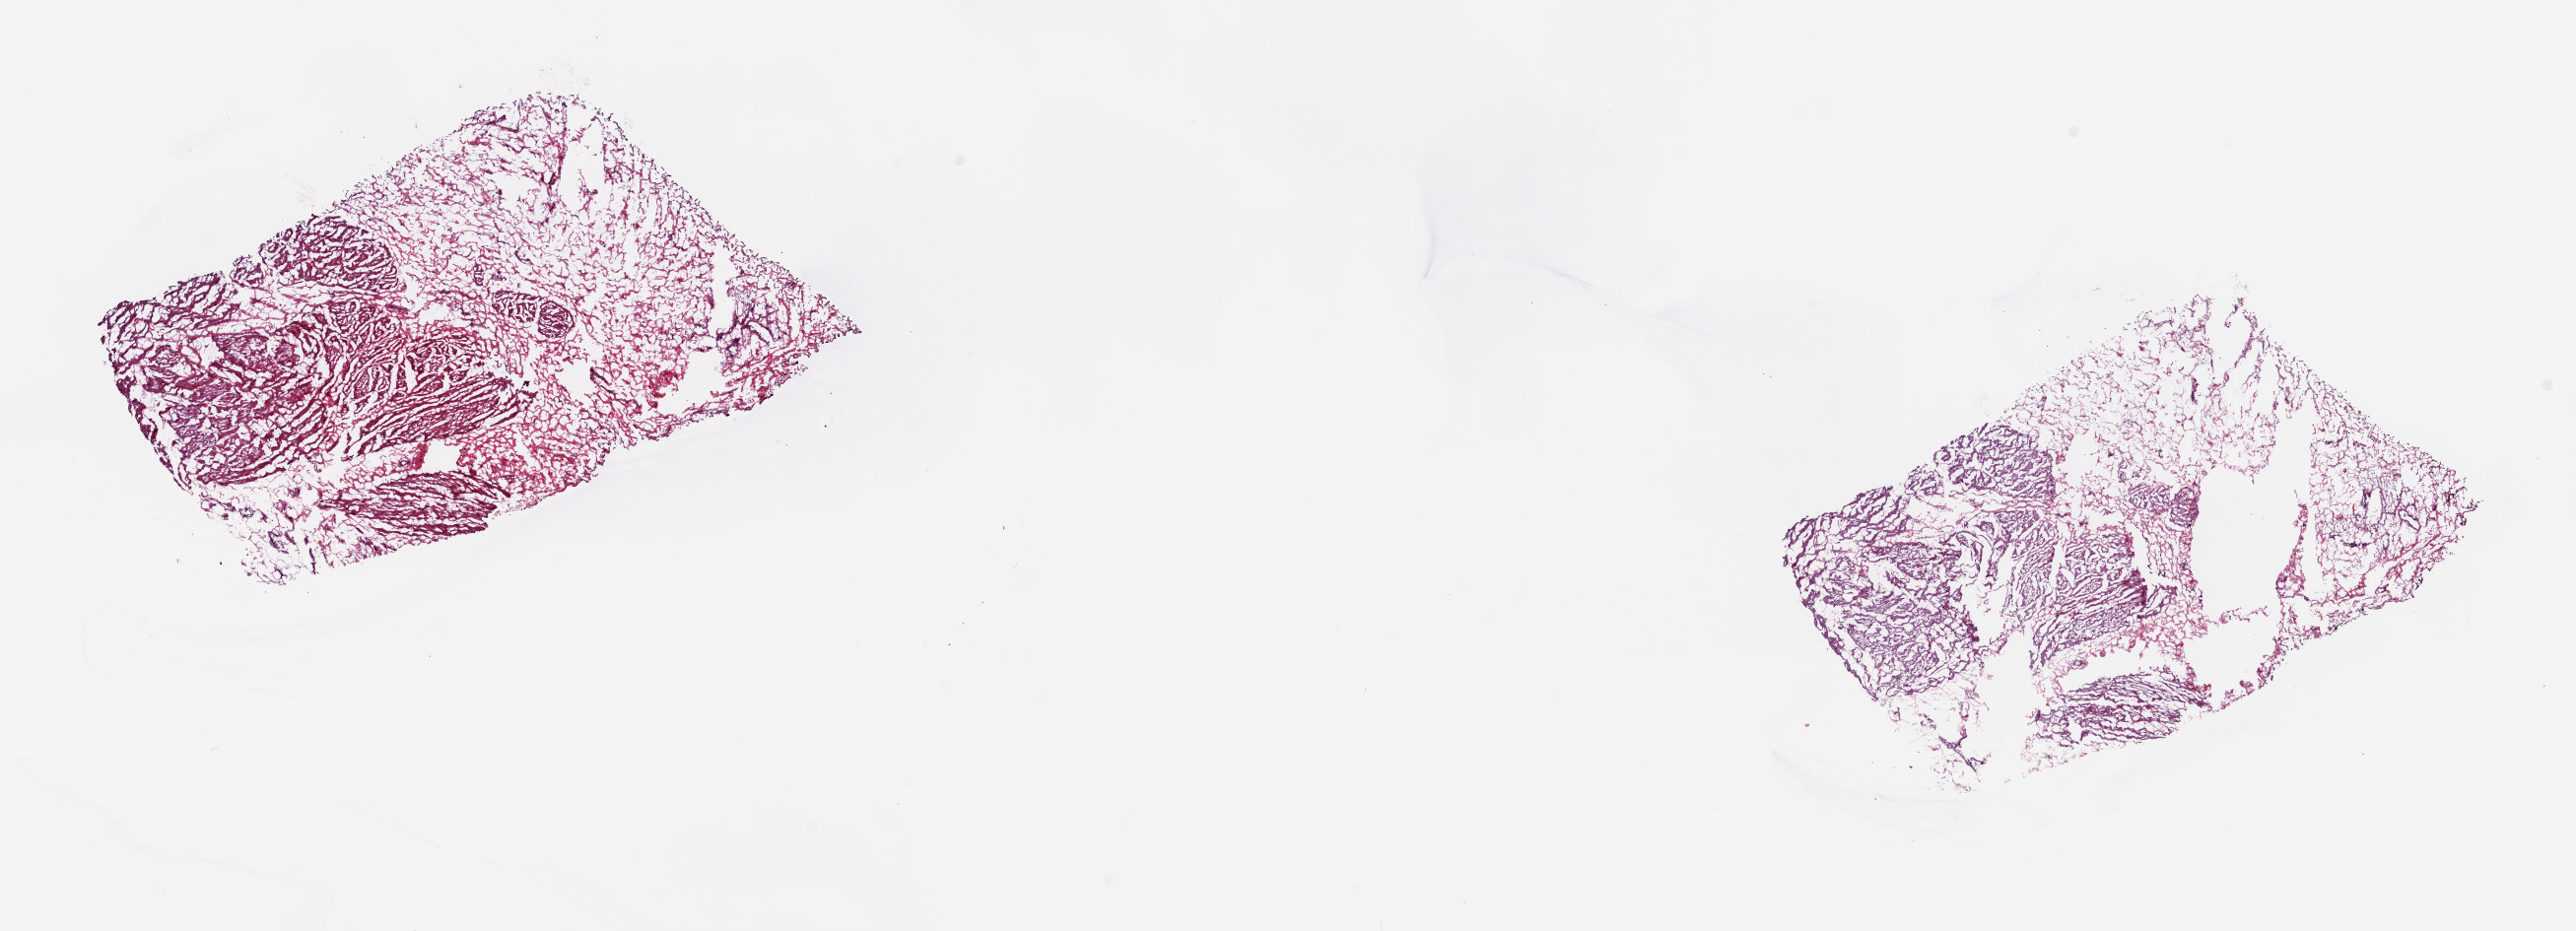
Digitized H&E tissue section (whole slide) — a low-resolution overview of the entire scanned area, about 20.8 x 7.5 mm (slide scanned at 20x); frozen section; sample: solid tissue normal (non-tumour tissue), bladder. Male, age 71 years at initial diagnosis. Pathologist review of this section (percent, as recorded): tumour cells 0%, tumour nuclei 0%.
This section: solid tissue normal sample (biorepository sample class). Patient diagnosis: Transitional cell carcinoma (lateral wall of bladder).